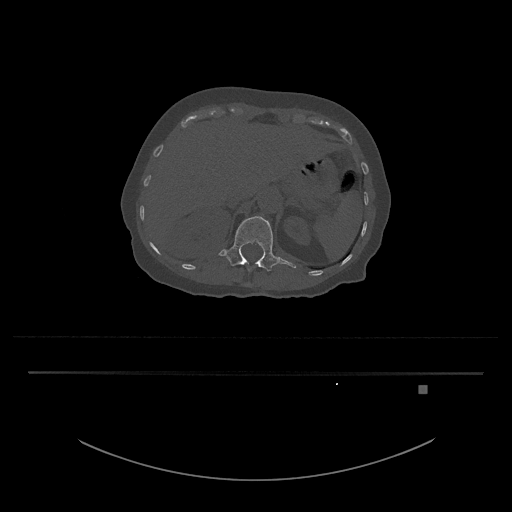
CT including the spine, one axial slice. Slice 560 of 797 in the series (ordered by position). Reconstruction kernel Br40s/3. 120 kVp. Bone window (W 1800 / L 400 HU). 0.5 mm slice thickness. 512 × 512 image matrix. Patient: female, 57 years. Case-level facts recorded for this patient, not image findings: primary cancer: cervical.
Structures marked on this image (semi-automatic segmentation, software-assisted and operator-edited):
- L1 vertebra: bounding box <219,216,296,272> (left, top, right, bottom; pixels)